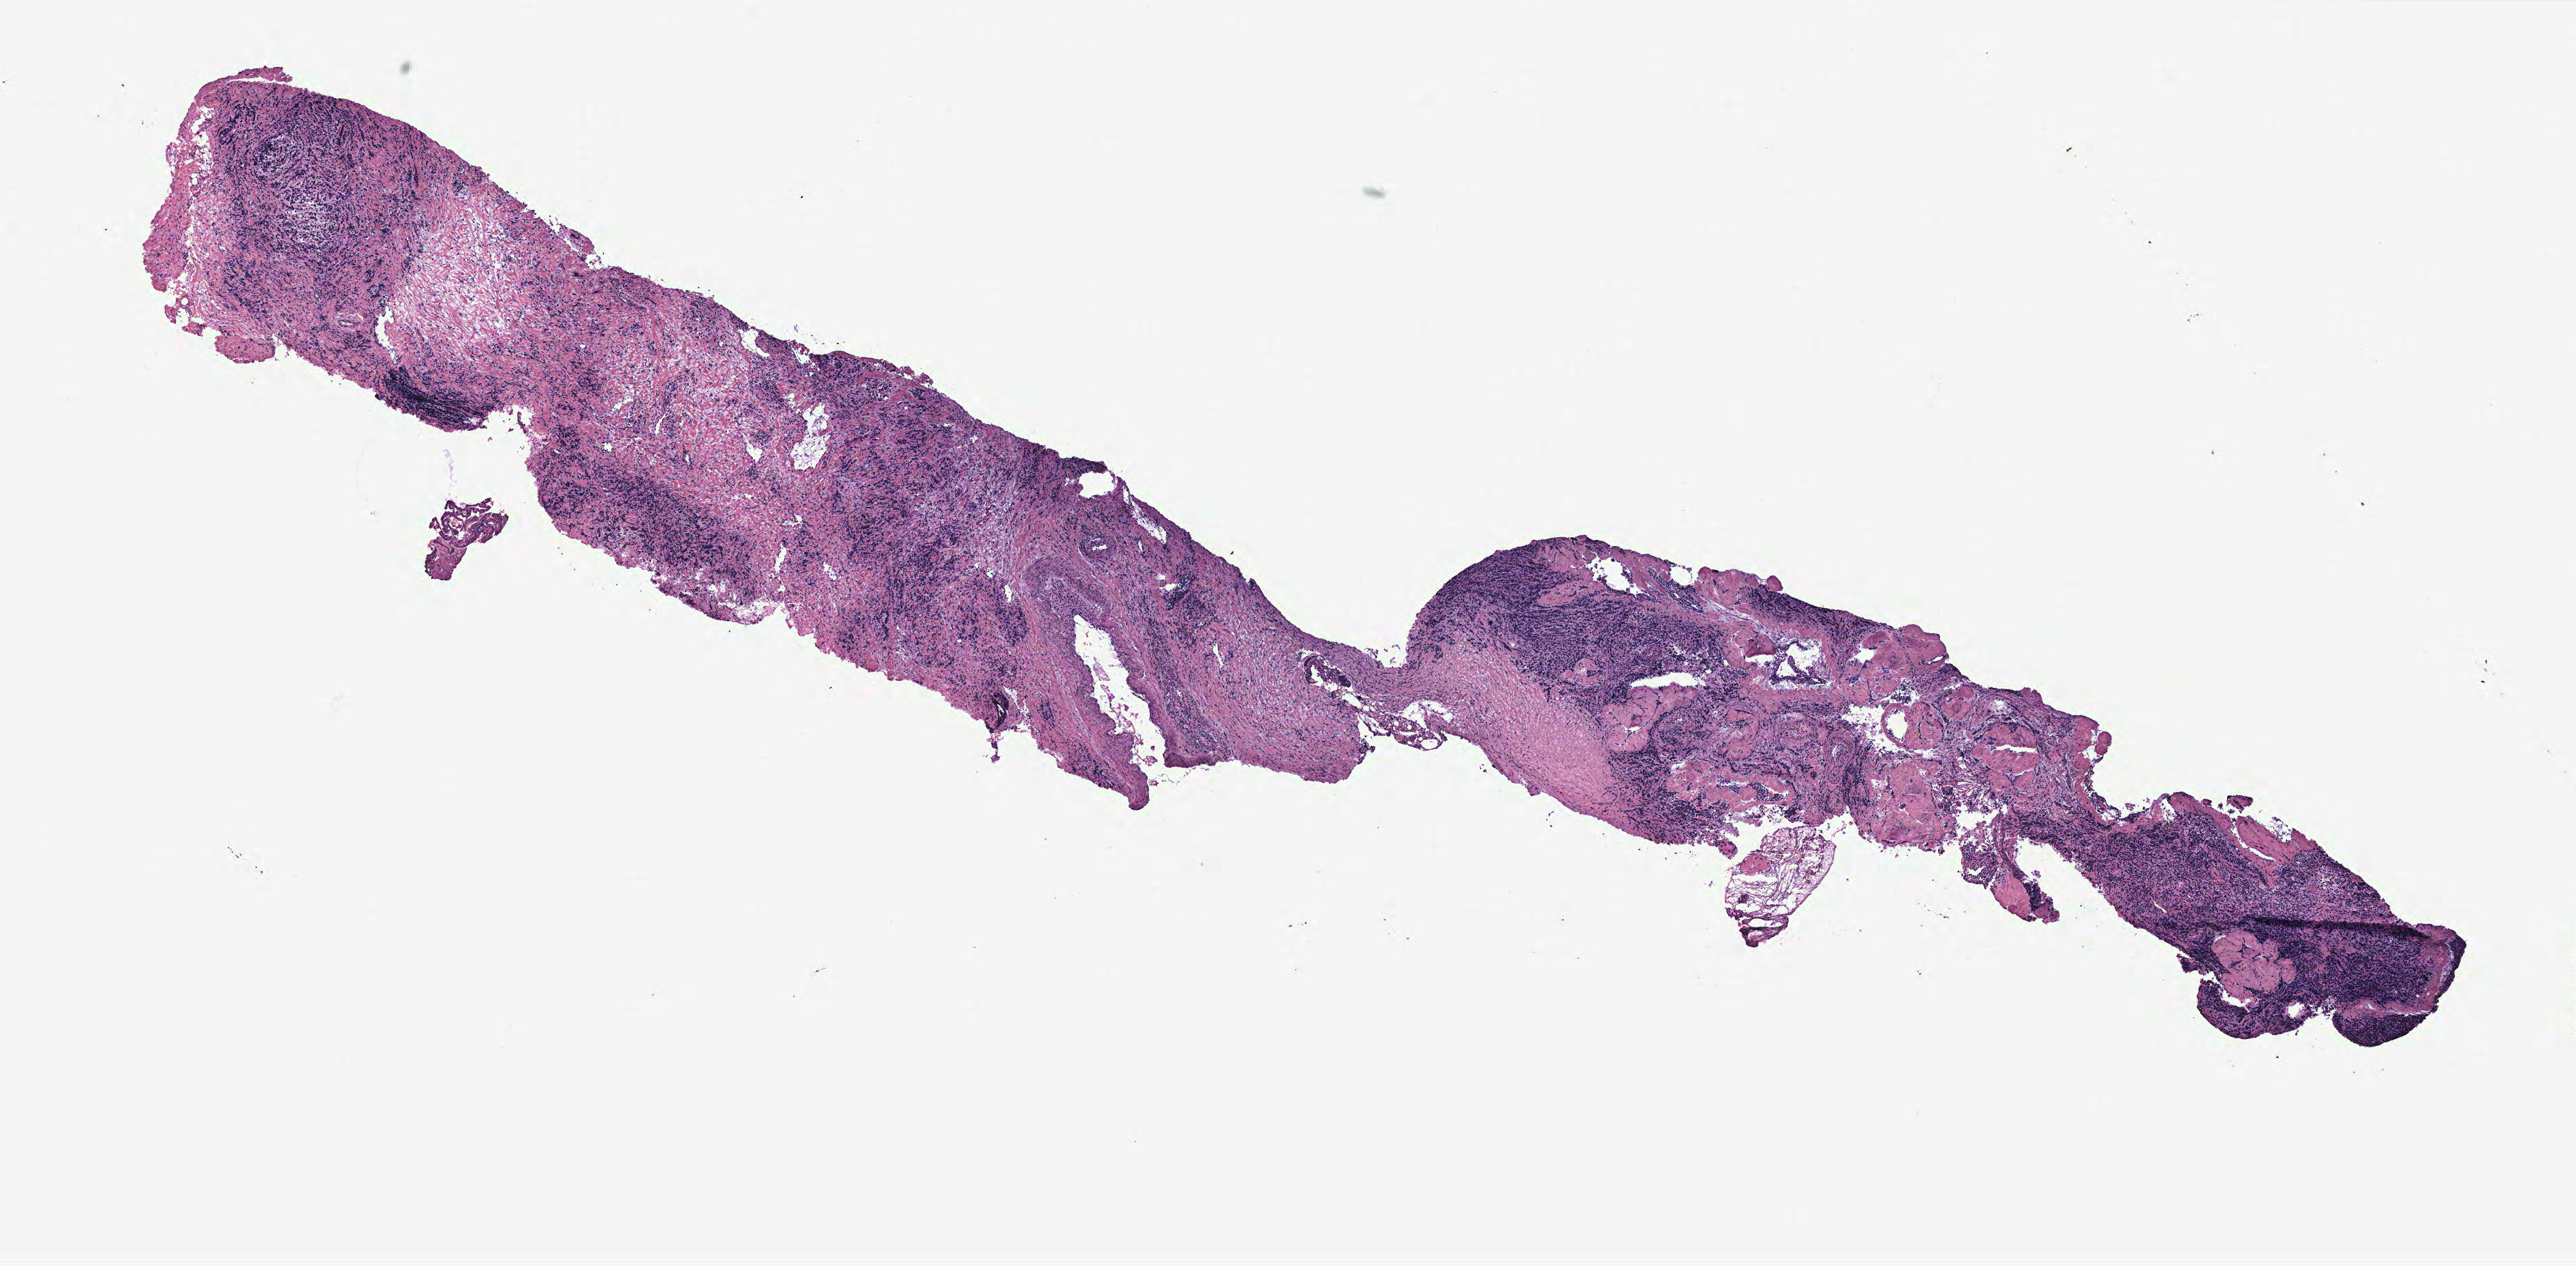
Digitized H&E tissue section (whole slide) — a low-resolution overview of the entire scanned area, about 15.1 x 7.4 mm (acquisition: 40x scan). Breast, tissue type not recorded. Female, 39 y/o.
Patient diagnosis: Infiltrating lobular carcinoma, NOS.